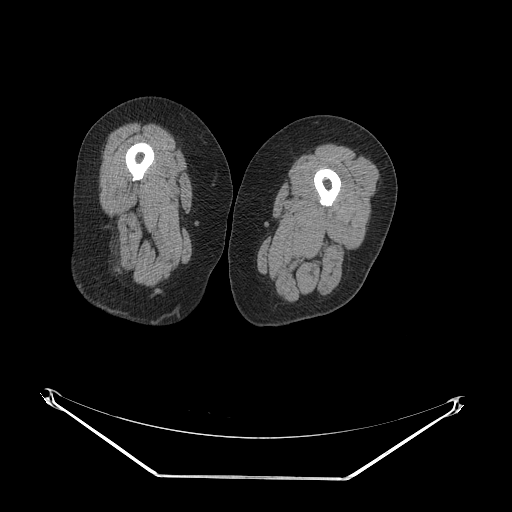
CT of an extremity soft-tissue mass (from a PET/CT study), one axial slice. Slice 18 of 257 in the series (ordered by position). Reconstruction kernel STANDARD. Soft-tissue window (W 400 / L 40 HU). 512 × 512 image matrix. Female patient. Case-level facts recorded for this patient, not image findings: histological type: synovial sarcoma; grade: intermediate; site of the primary tumour: right buttock.
Structures marked on this image (expert contour drawn on MRI and transferred to this co-registered scan by the dataset authors):
- gross tumour volume including surrounding oedema: bounding box <103,263,113,275> (left, top, right, bottom; pixels)